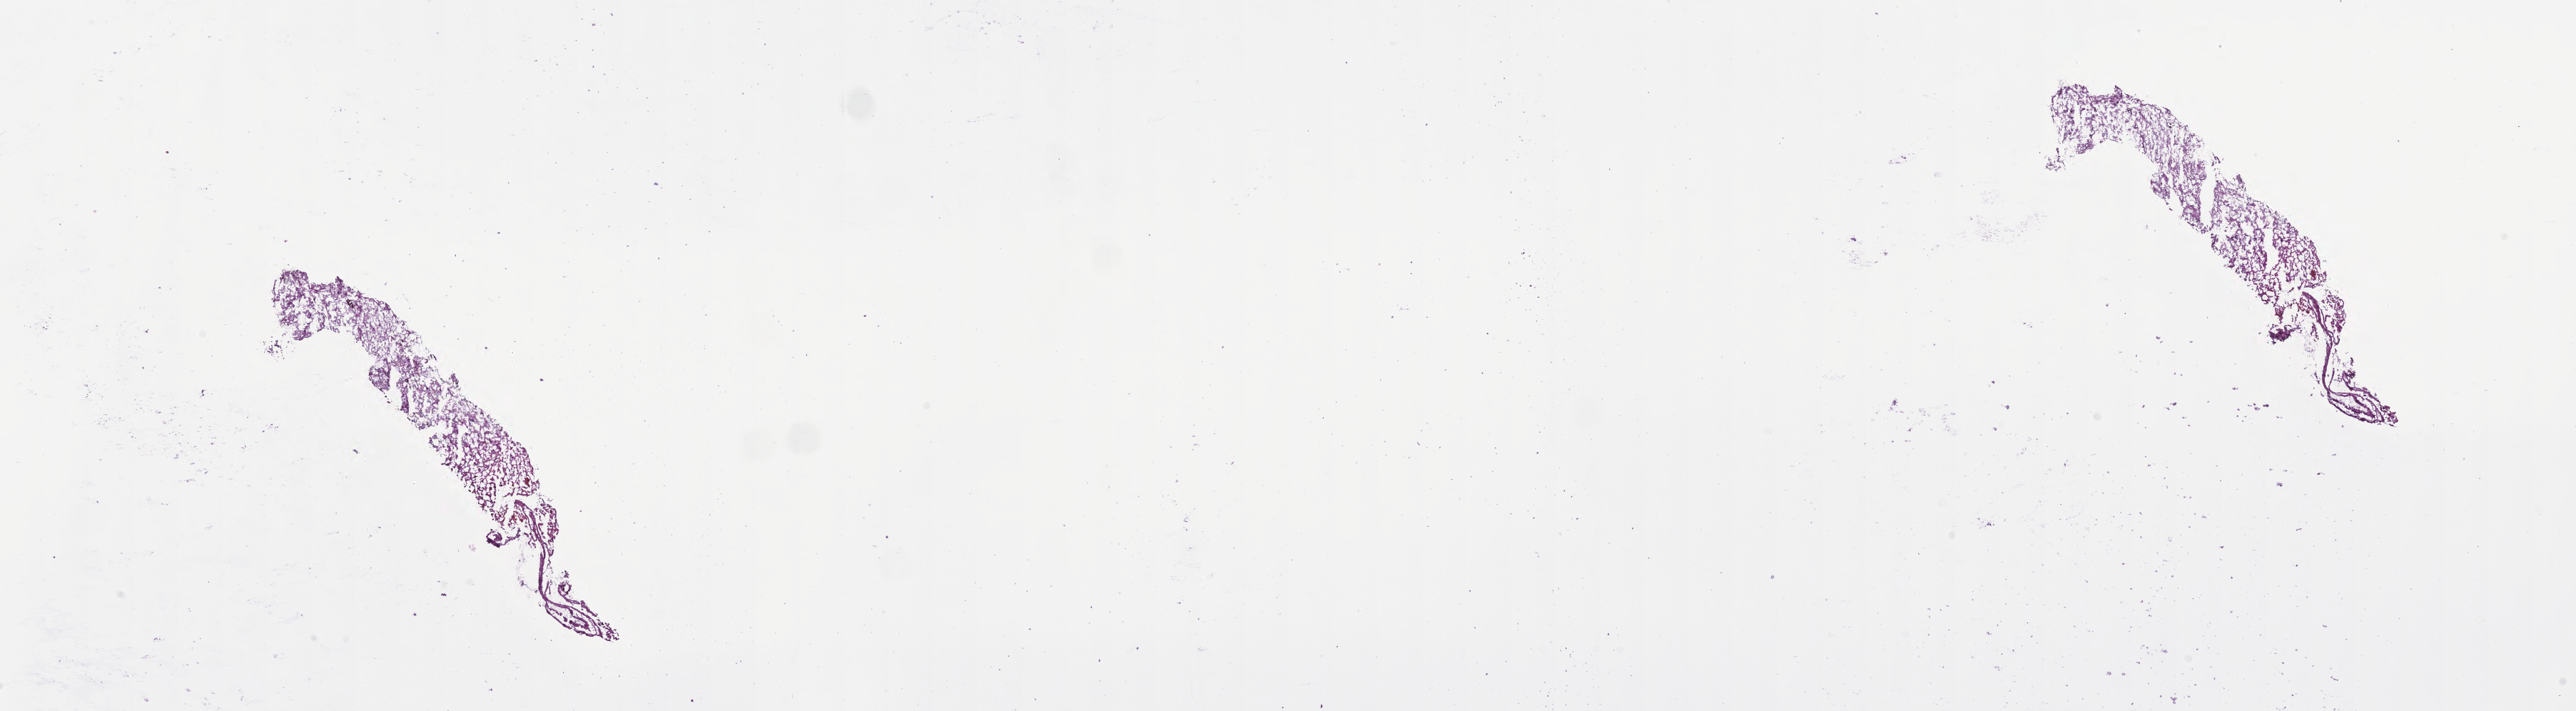
Digitized hematoxylin and eosin (H&E)-stained section of tumor tissue from the brain — low-resolution overview of the scanned area, about 29.2 x 8.1 mm. Frozen section (OCT-embedded). Male patient, age 115 months (9 years 7 months).
Diagnosis: Pilocytic astrocytoma.